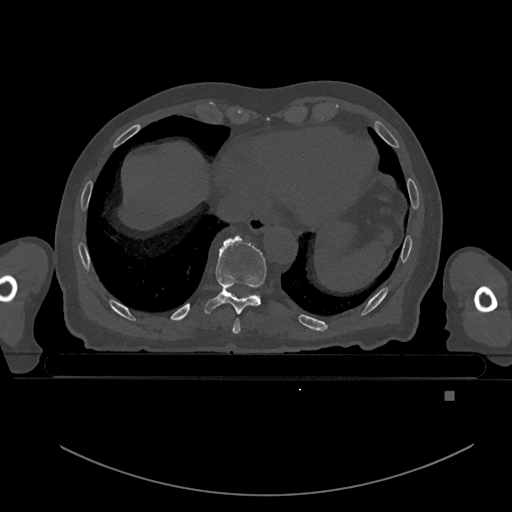
CT including the spine, one axial slice. Position 143 of 969 along the scan axis. Bone window (W 1800 / L 400 HU). 512 × 512 image matrix, field of view 456 × 456 mm. Male patient, age 82 years. Case-level facts recorded for this patient, not image findings: primary cancer: prostate; vertebrae with lytic lesions (as recorded): T11, T9, T8, T2.
Outlined on this slice (semi-automatic segmentation, software-assisted and operator-edited):
- T8 vertebra: bounding box <232,318,241,334> (left, top, right, bottom; pixels)
- T9 vertebra: <204,236,267,314>